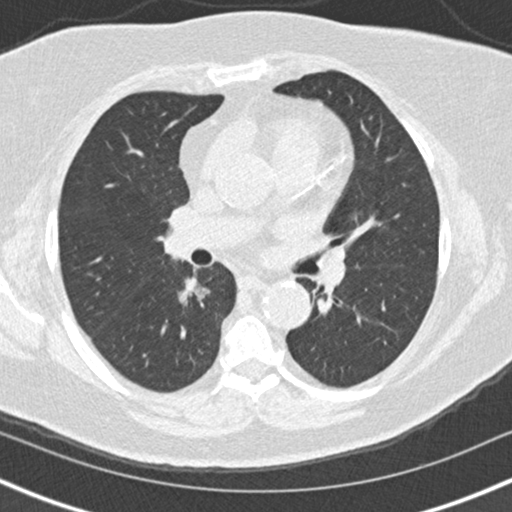
Low-dose screening chest CT, one axial slice. Slice 88 of 152 in the series (ordered by position). 120 kVp. Lung window (W 1500 / L -600 HU). 2 mm slice thickness. 512 × 512 image matrix, field of view 320 × 320 mm.
Outlined on this slice (outlined manually by an expert reader):
- lesion 1 (tumor, lower lobe of right lung): box from (x=178, y=276) to (x=210, y=306) px